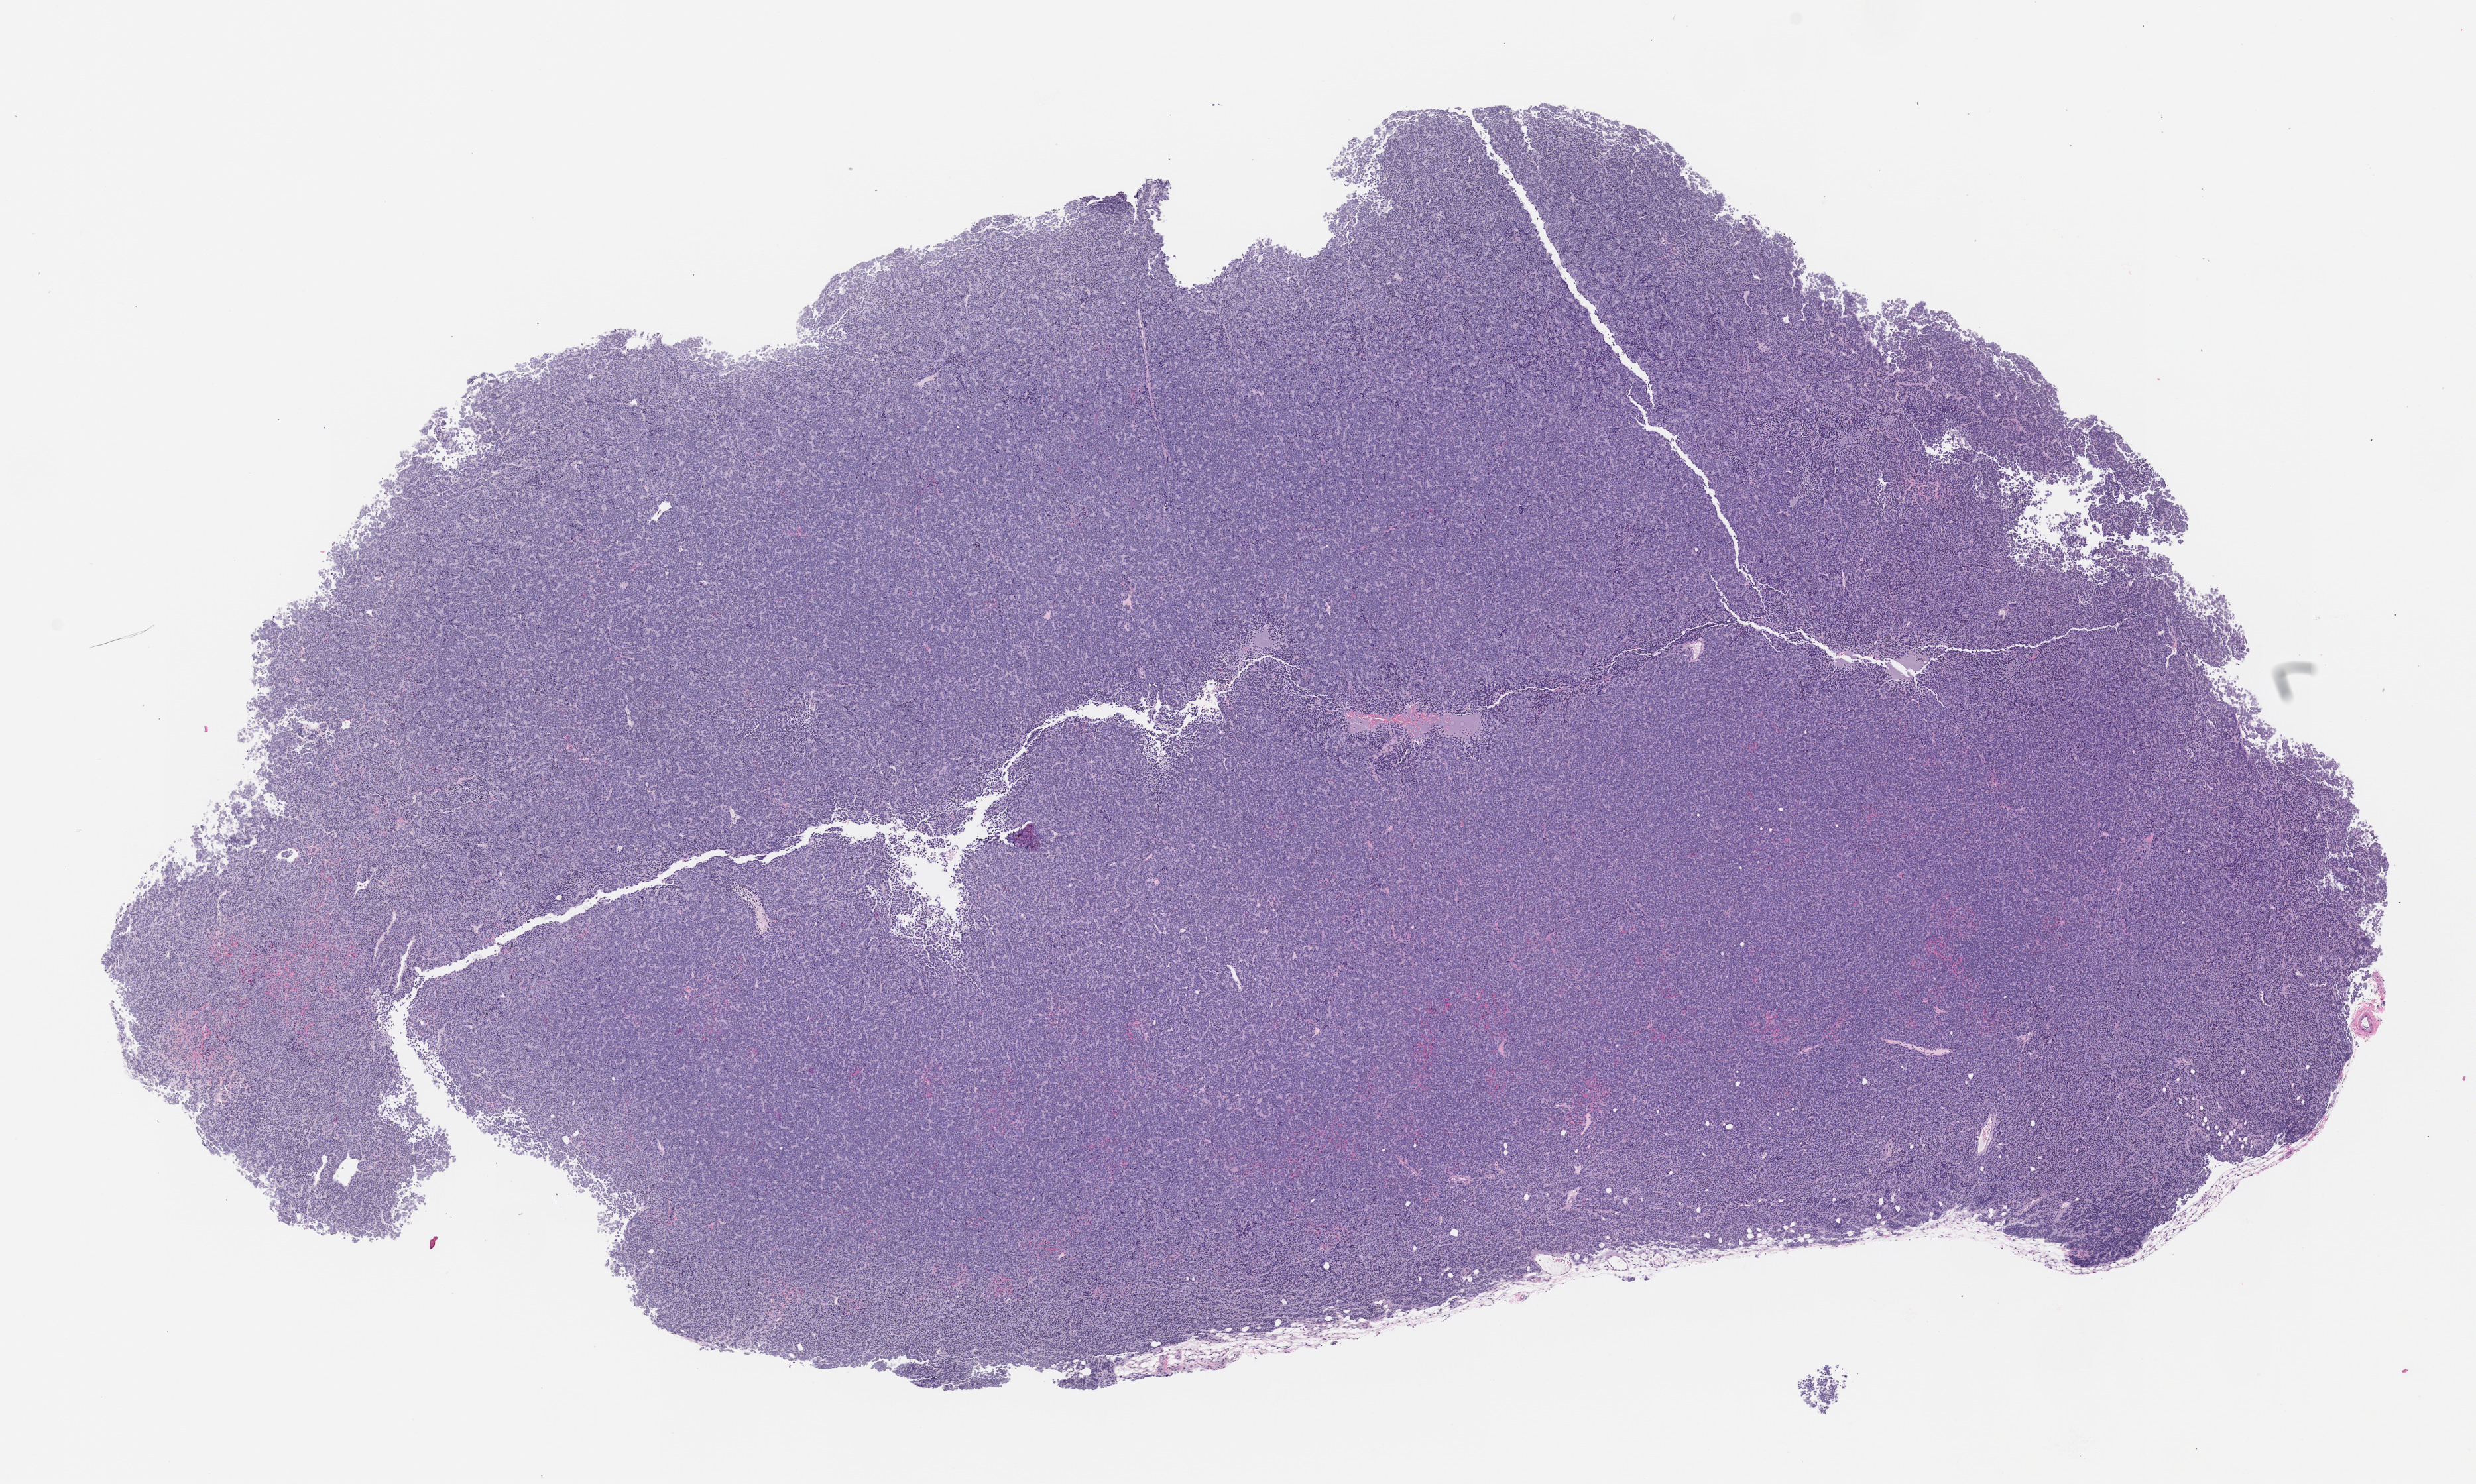
Whole-slide image, H&E: patient-derived xenograft (human tumor grown in a mouse), passage 1 — whole scanned area (about 15.0 x 9.0 mm) shown as a low-resolution overview. Formalin-fixed, paraffin-embedded (FFPE) tissue. Tumor site category: musculoskeletal.
Originating patient diagnosis: Ewing Sarcoma|Primitive Neuroectodermal Tumor.